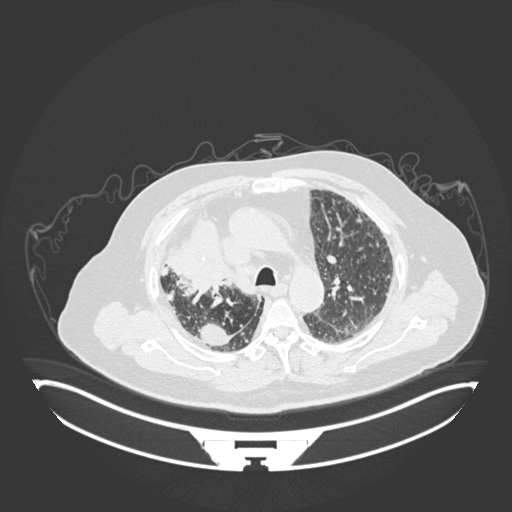
Chest CT, one axial slice. Slice 127 of 201 in the series (ordered by position). Lung window (W 1500 / L -600 HU). 1 mm slice thickness. 512 × 512 image matrix, field of view 500 × 500 mm. Male patient, age 69 years. Case-level facts recorded for this patient, not image findings: clinical TNM (as recorded): T4 N3 M1.
Structures marked on this image (bounding box drawn by a radiologist):
- lung tumour (recorded histology: adenocarcinoma): bounding box <161,209,238,293> (left, top, right, bottom; pixels)